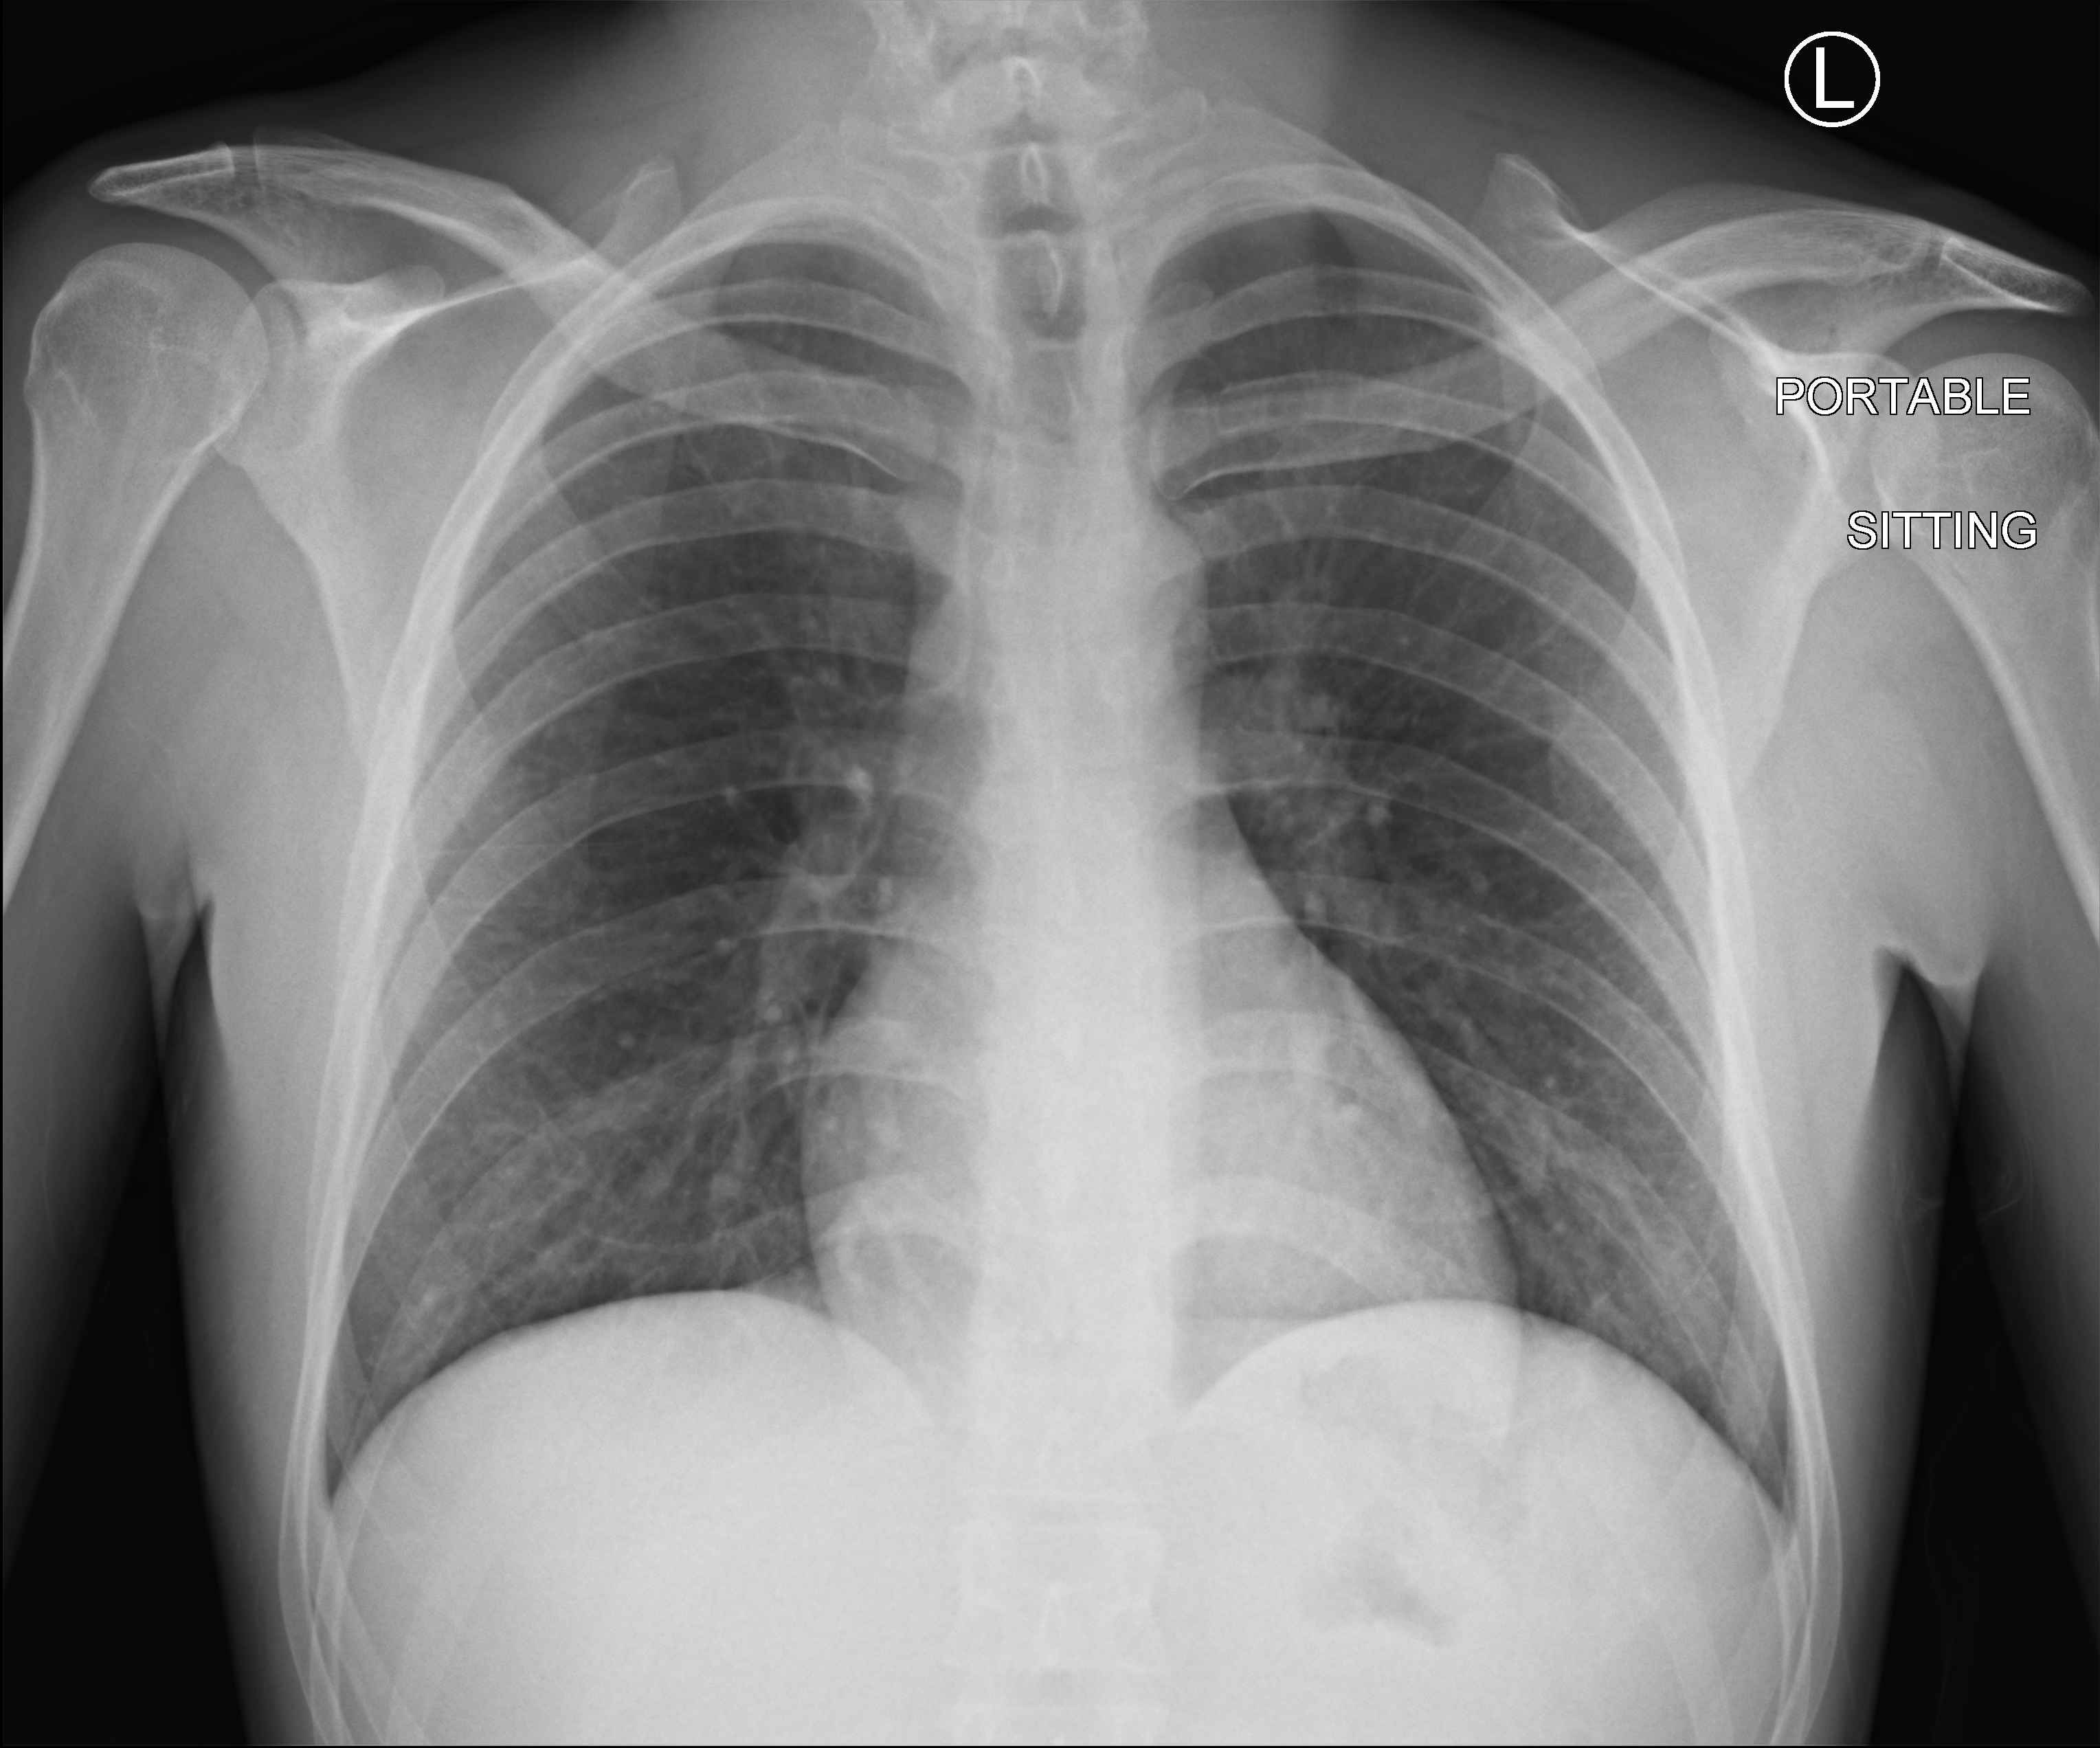
Bedside chest radiograph (computed radiography); anteroposterior (AP) projection. Male patient hospitalised with COVID-19, age 18–59 years.
Admission-level facts for this patient (not findings on this image; timing relative to this image not recorded): other chronic lung disease (admission record): yes; mechanically ventilated during this hospital stay: no.